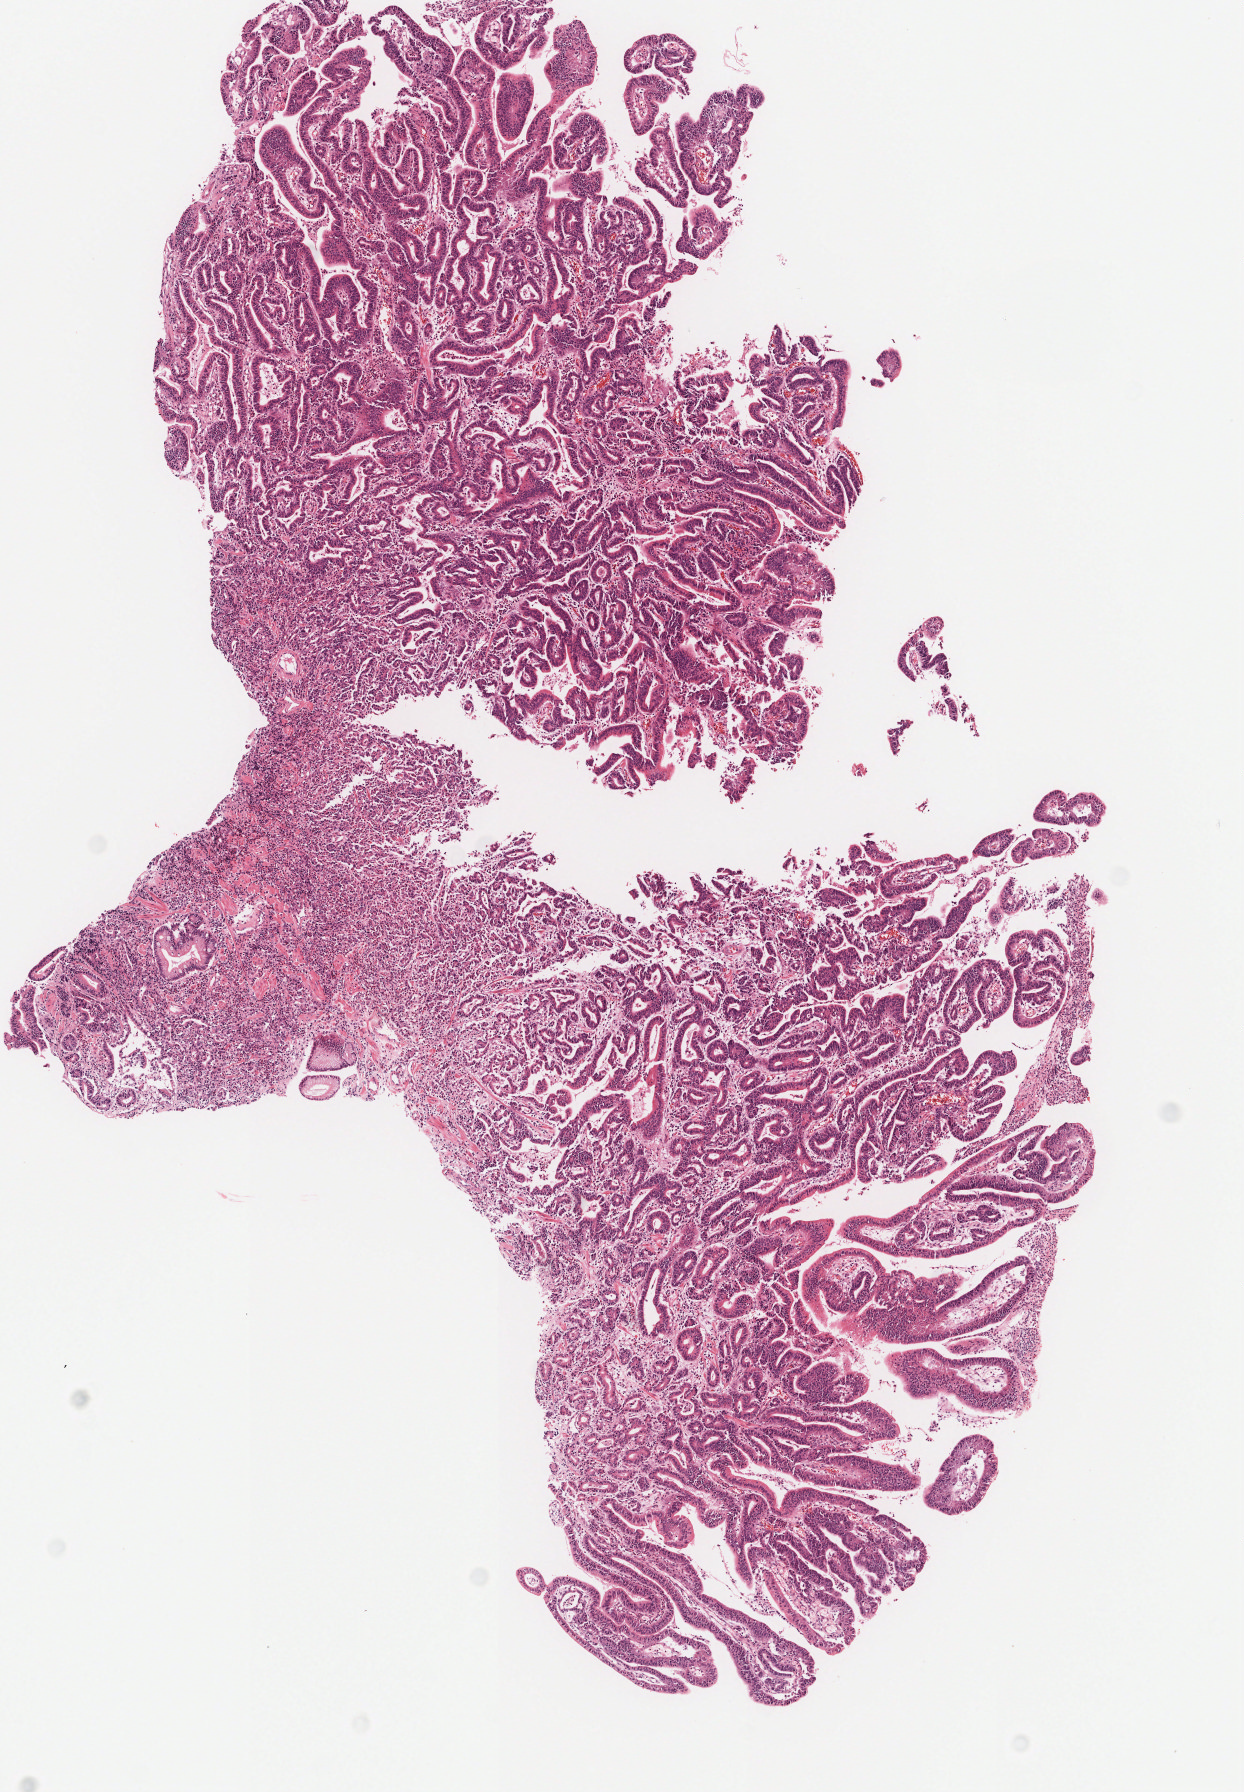
Hematoxylin and eosin (H&E) stained whole-slide image, shown as a low-resolution overview of the whole scanned area (about 4.9 x 7.1 mm, acquisition: 20x scan), formalin-fixed paraffin-embedded (FFPE) diagnostic section, primary tumour sample from the stomach. Female patient; age at initial diagnosis 67 years. Histologic grade: G2 (moderately differentiated).
Lymph nodes positive (case pathology): 0 of 42 examined. Pathologic diagnosis: Tubular adenocarcinoma (body of stomach). AJCC pathologic stage: IA.